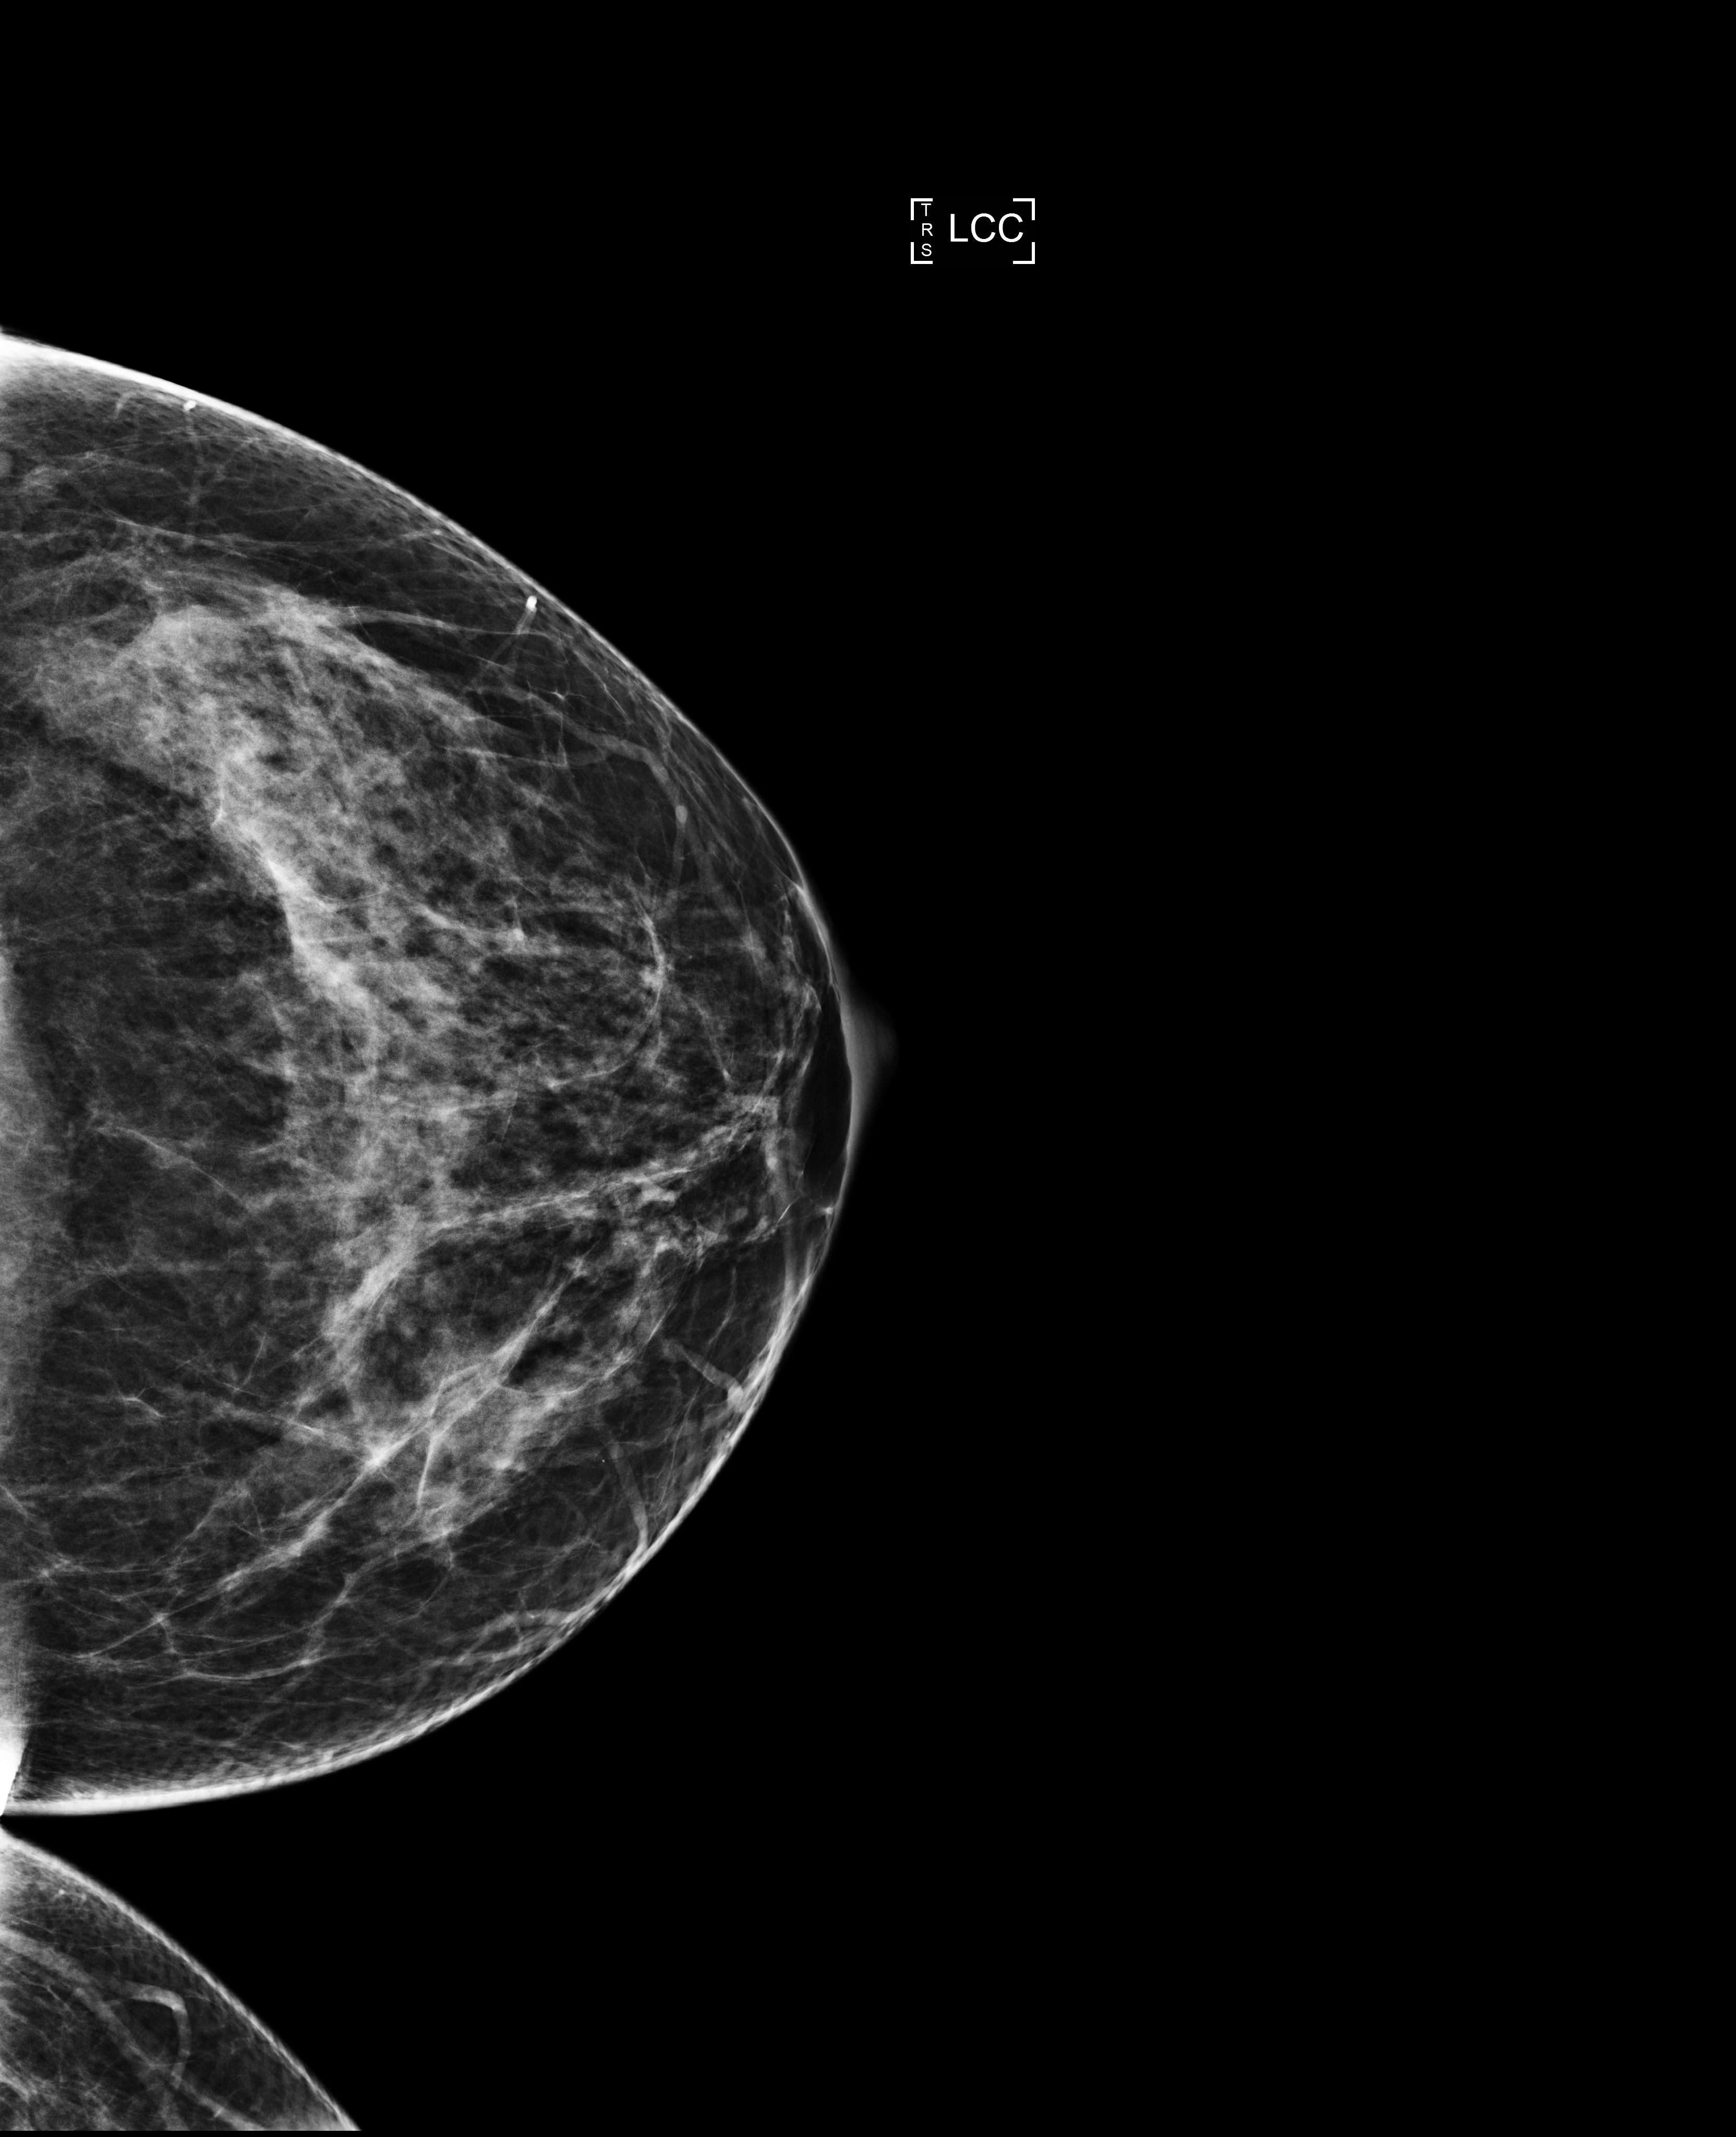
Digital mammogram (FFDM), left breast, craniocaudal (CC) view, screening examination, compressed breast thickness 68 mm. Patient aged 44 years (female).
Final BI-RADS category for the screening round (tomosynthesis exam, both breasts): category 2.